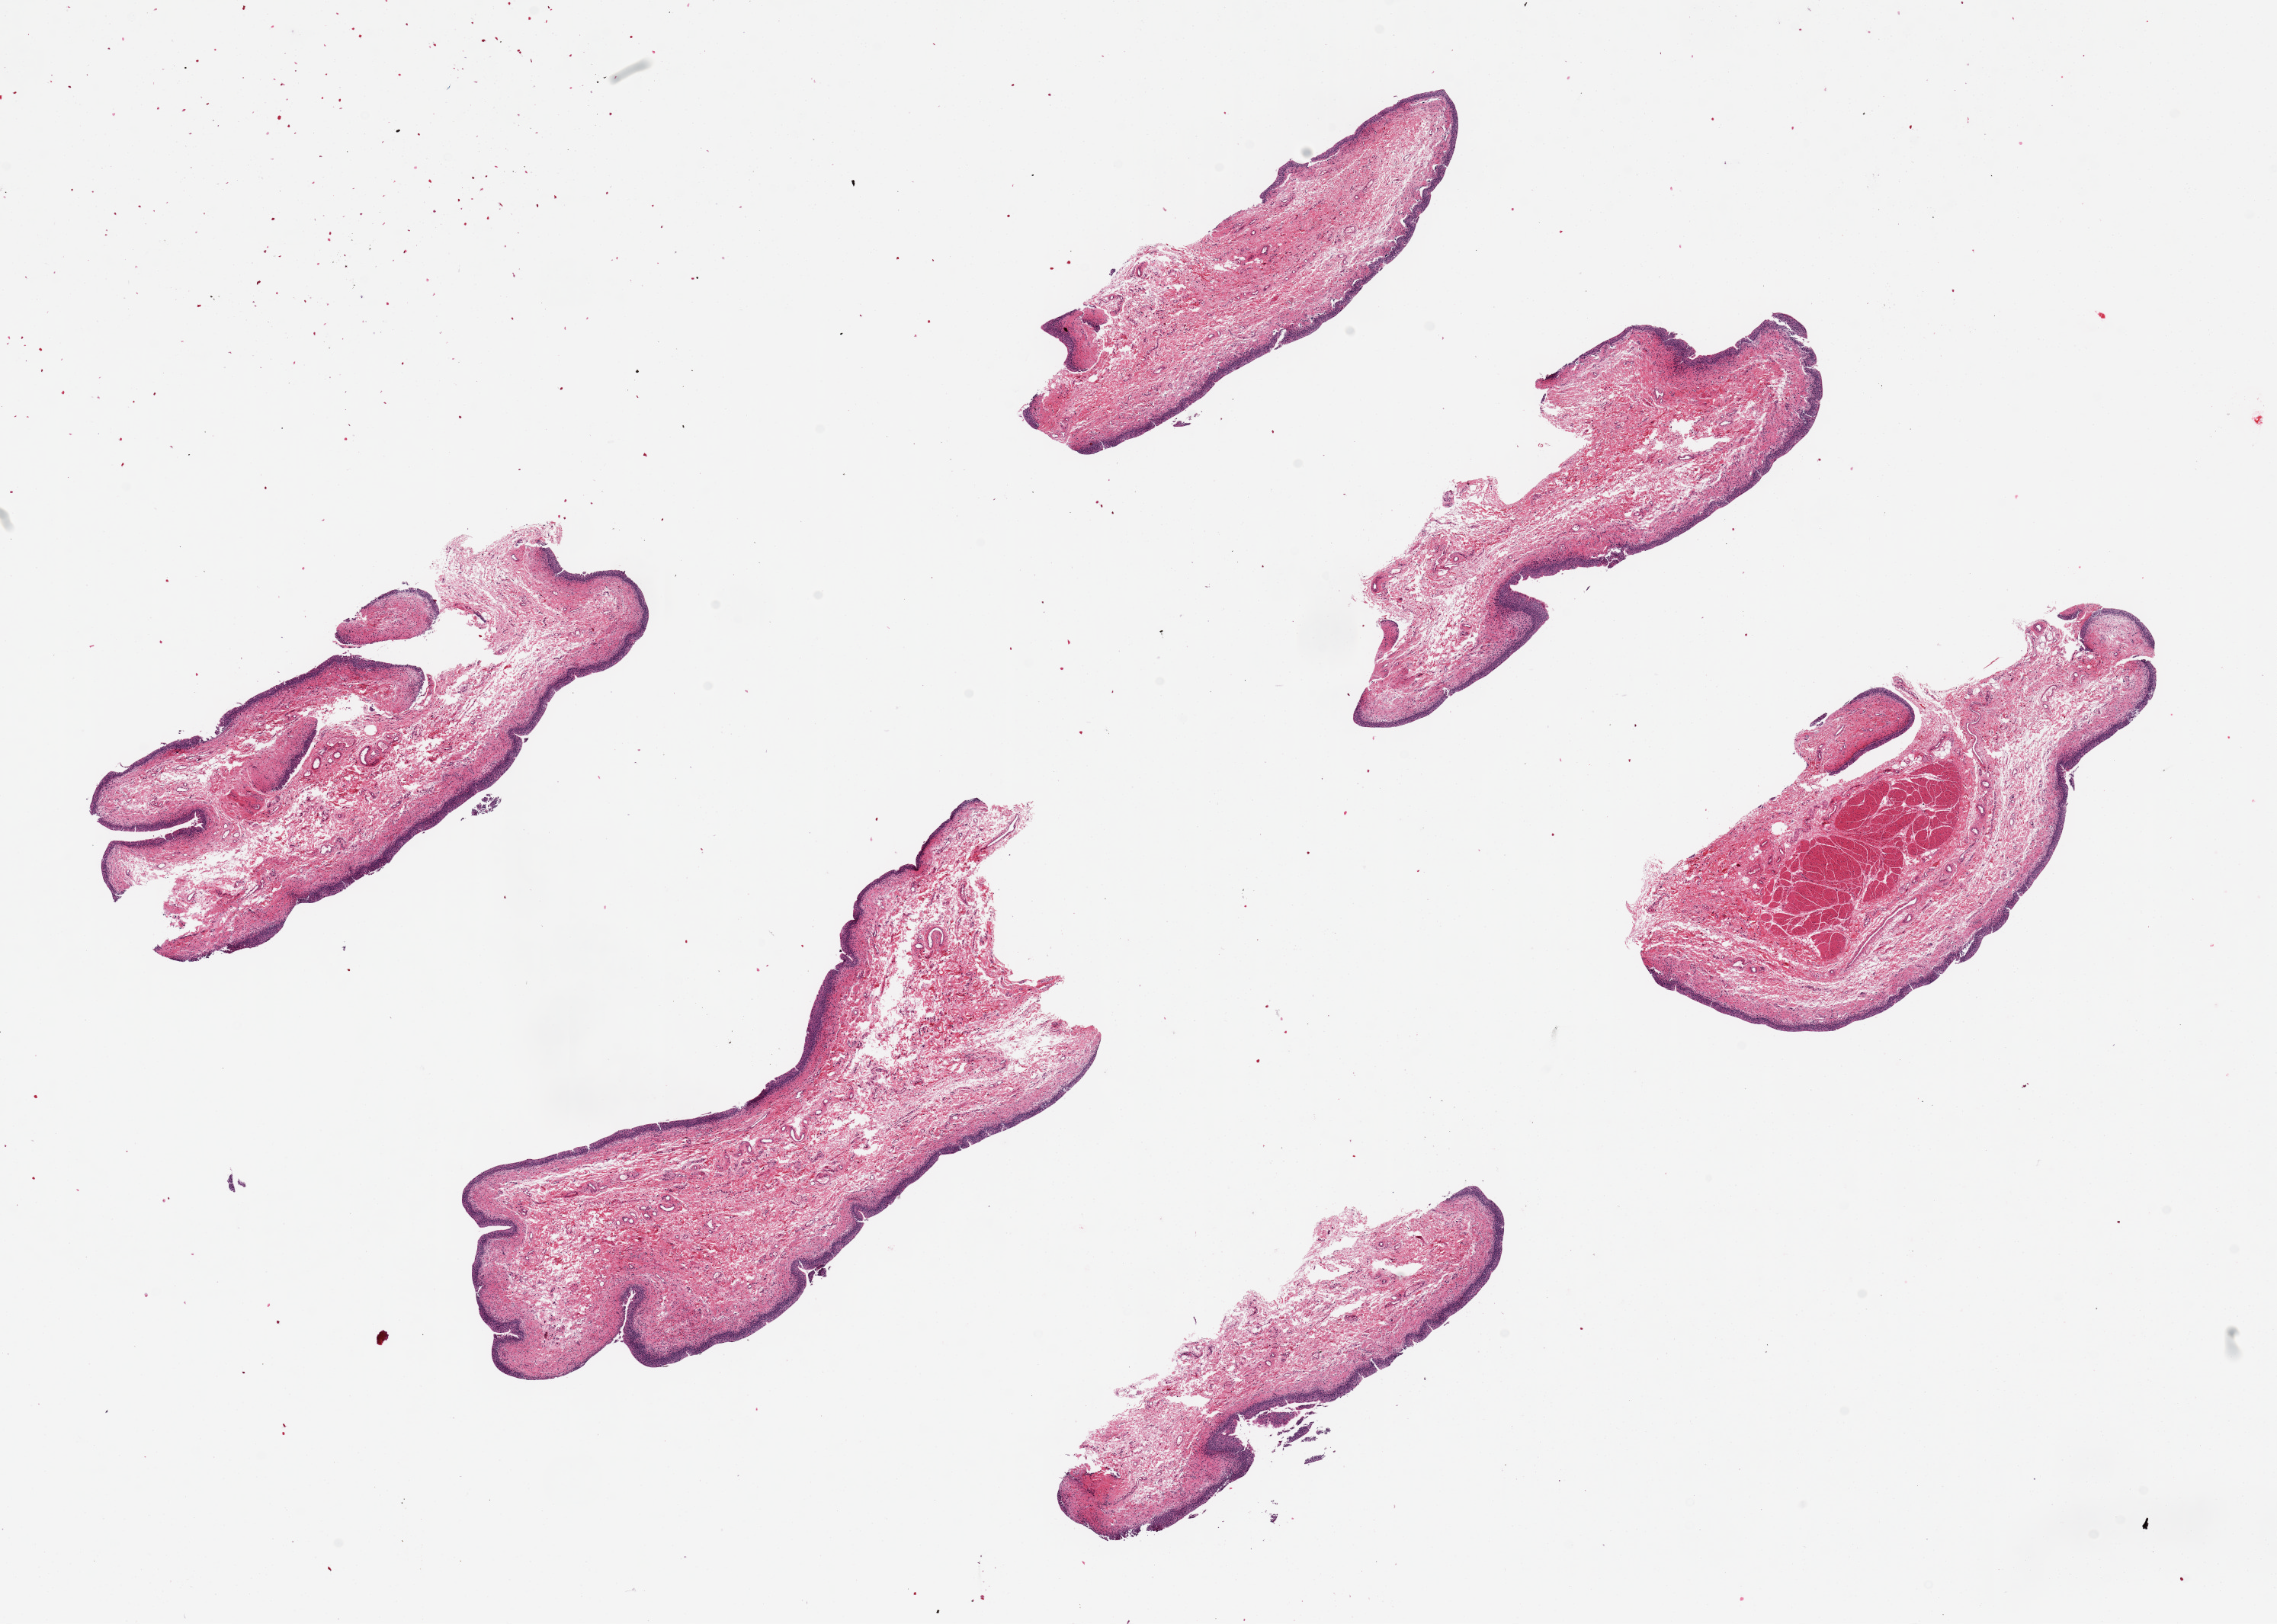
H&E whole-slide image — shown as a low-resolution overview of the whole scanned area (about 23.6 x 16.9 mm, from a 20x scan). PAXgene-fixed paraffin-embedded (PFPE) section. Sampled site (target tissue): urinary bladder. Donor tissue sample. Male donor.
• review note (as recorded): 6 pieces up to 7 x2.7 mm; good mucosa; muscle in one piece; edematous stroma